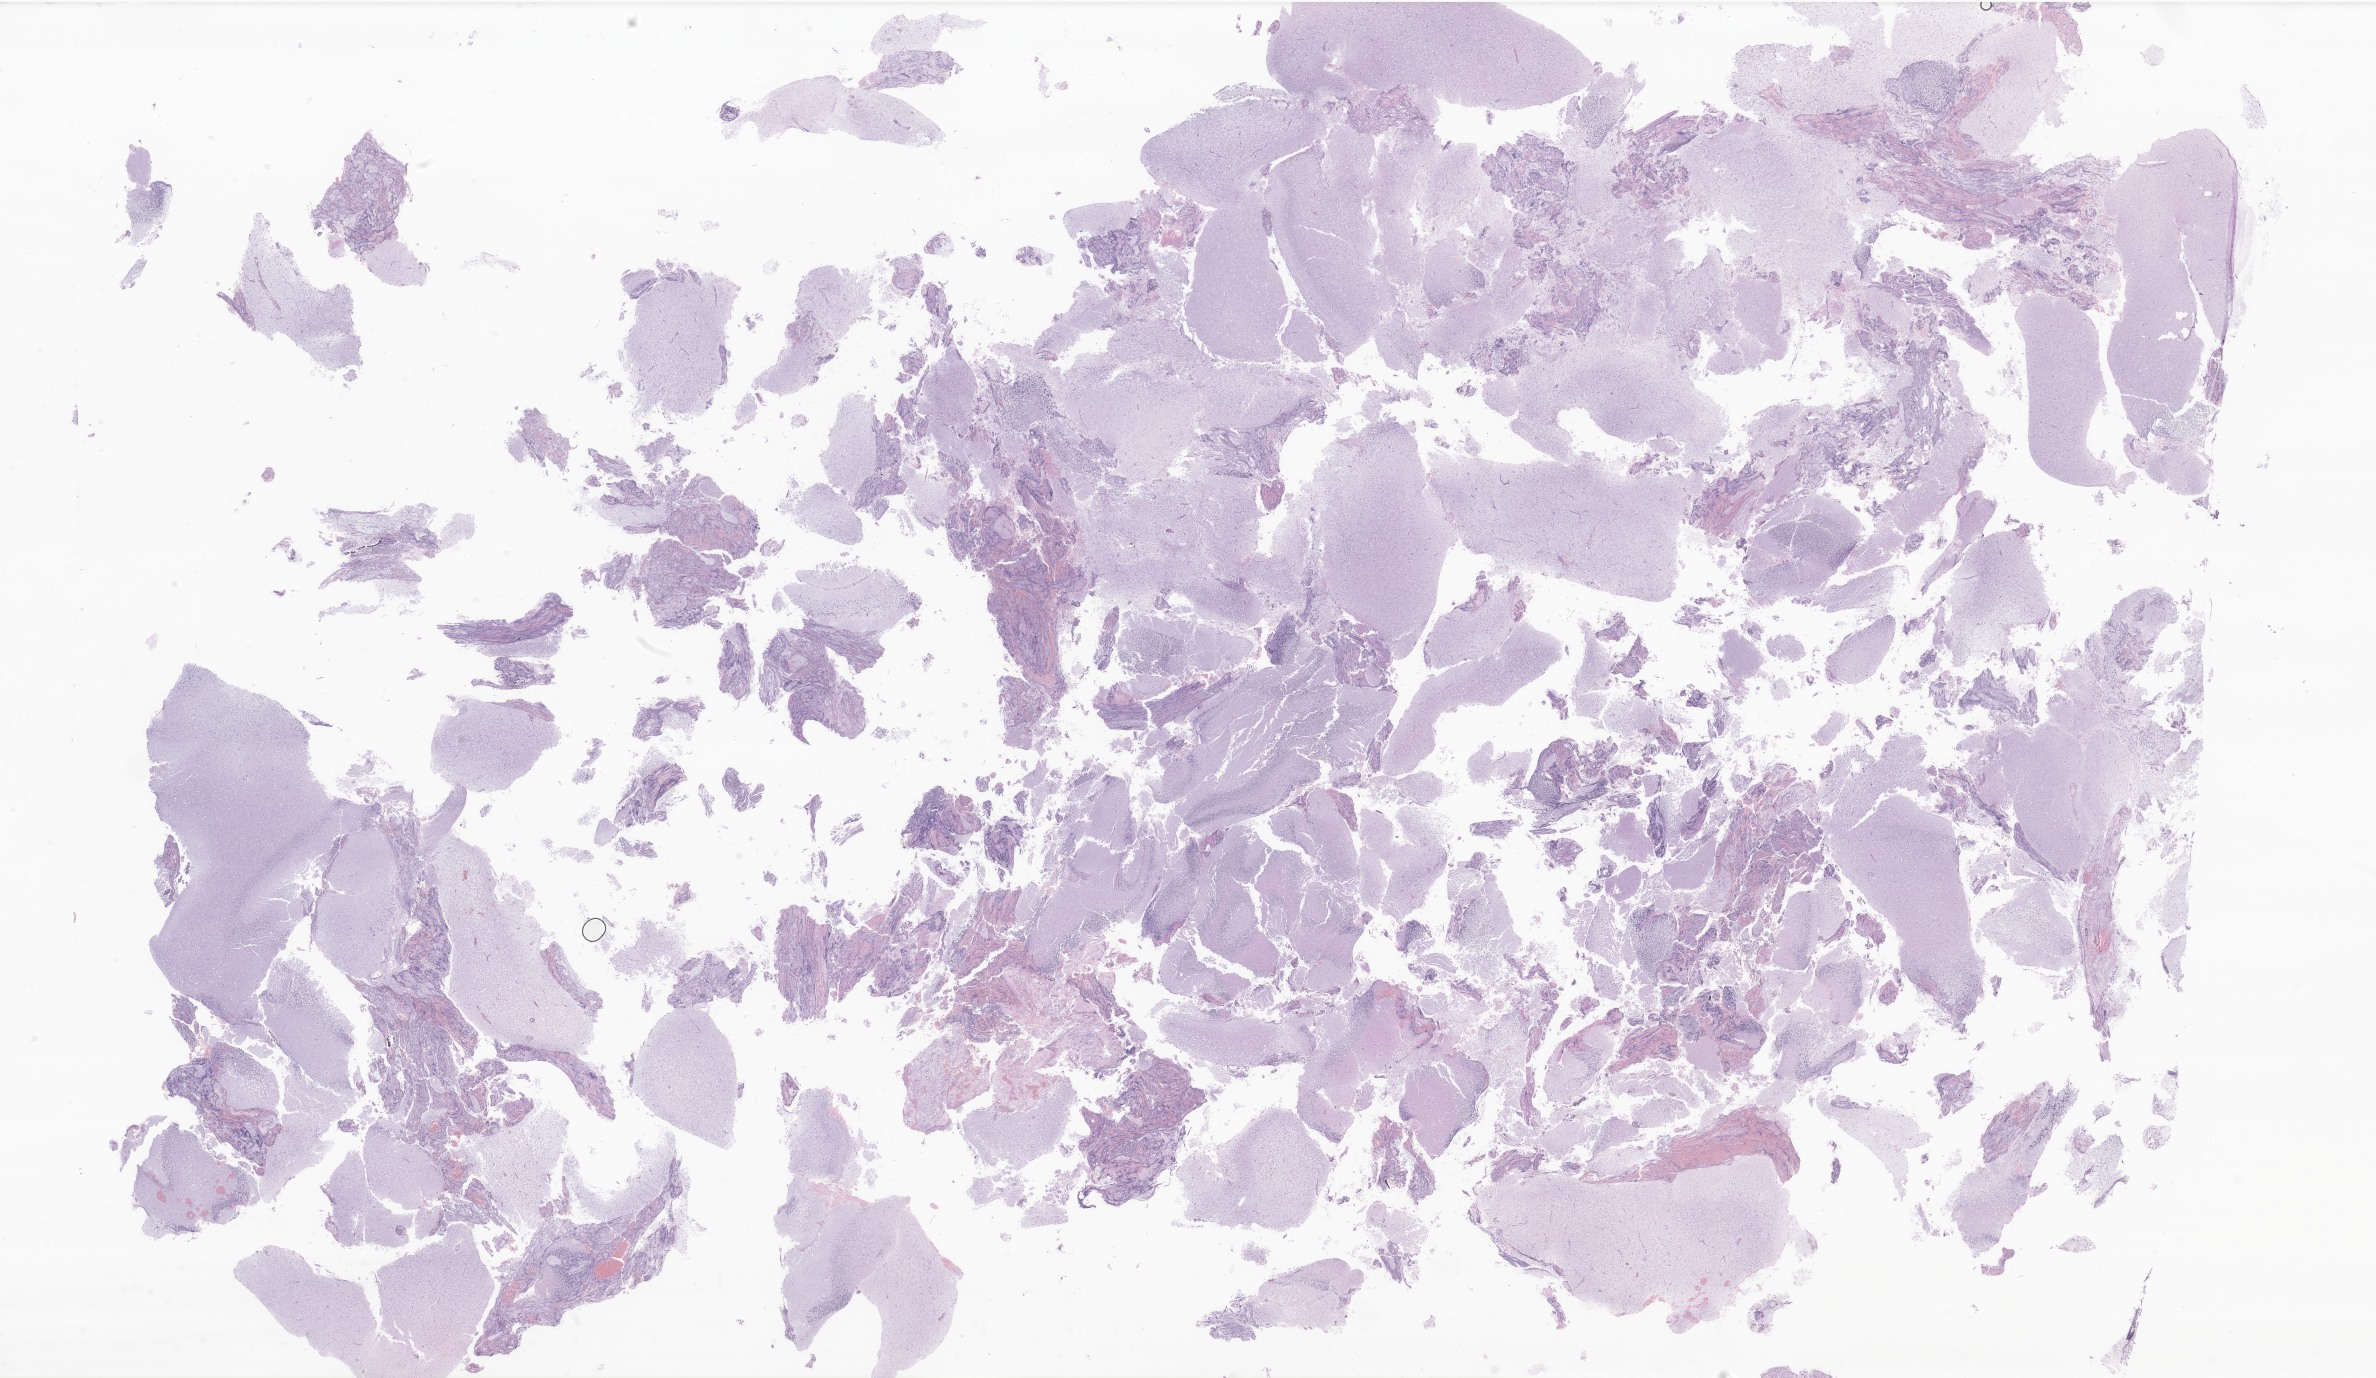
Hematoxylin and eosin (H&E) whole-slide image of tumor tissue from the cerebrum, whole scanned area (about 40.1 x 23.2 mm) shown as a low-resolution overview. Formalin-fixed, paraffin-embedded (FFPE) tissue. Patient male; age 722 days (about 2.0 years).
Diagnosis (ICD-O-3 morphology term): Pilocytic astrocytoma.